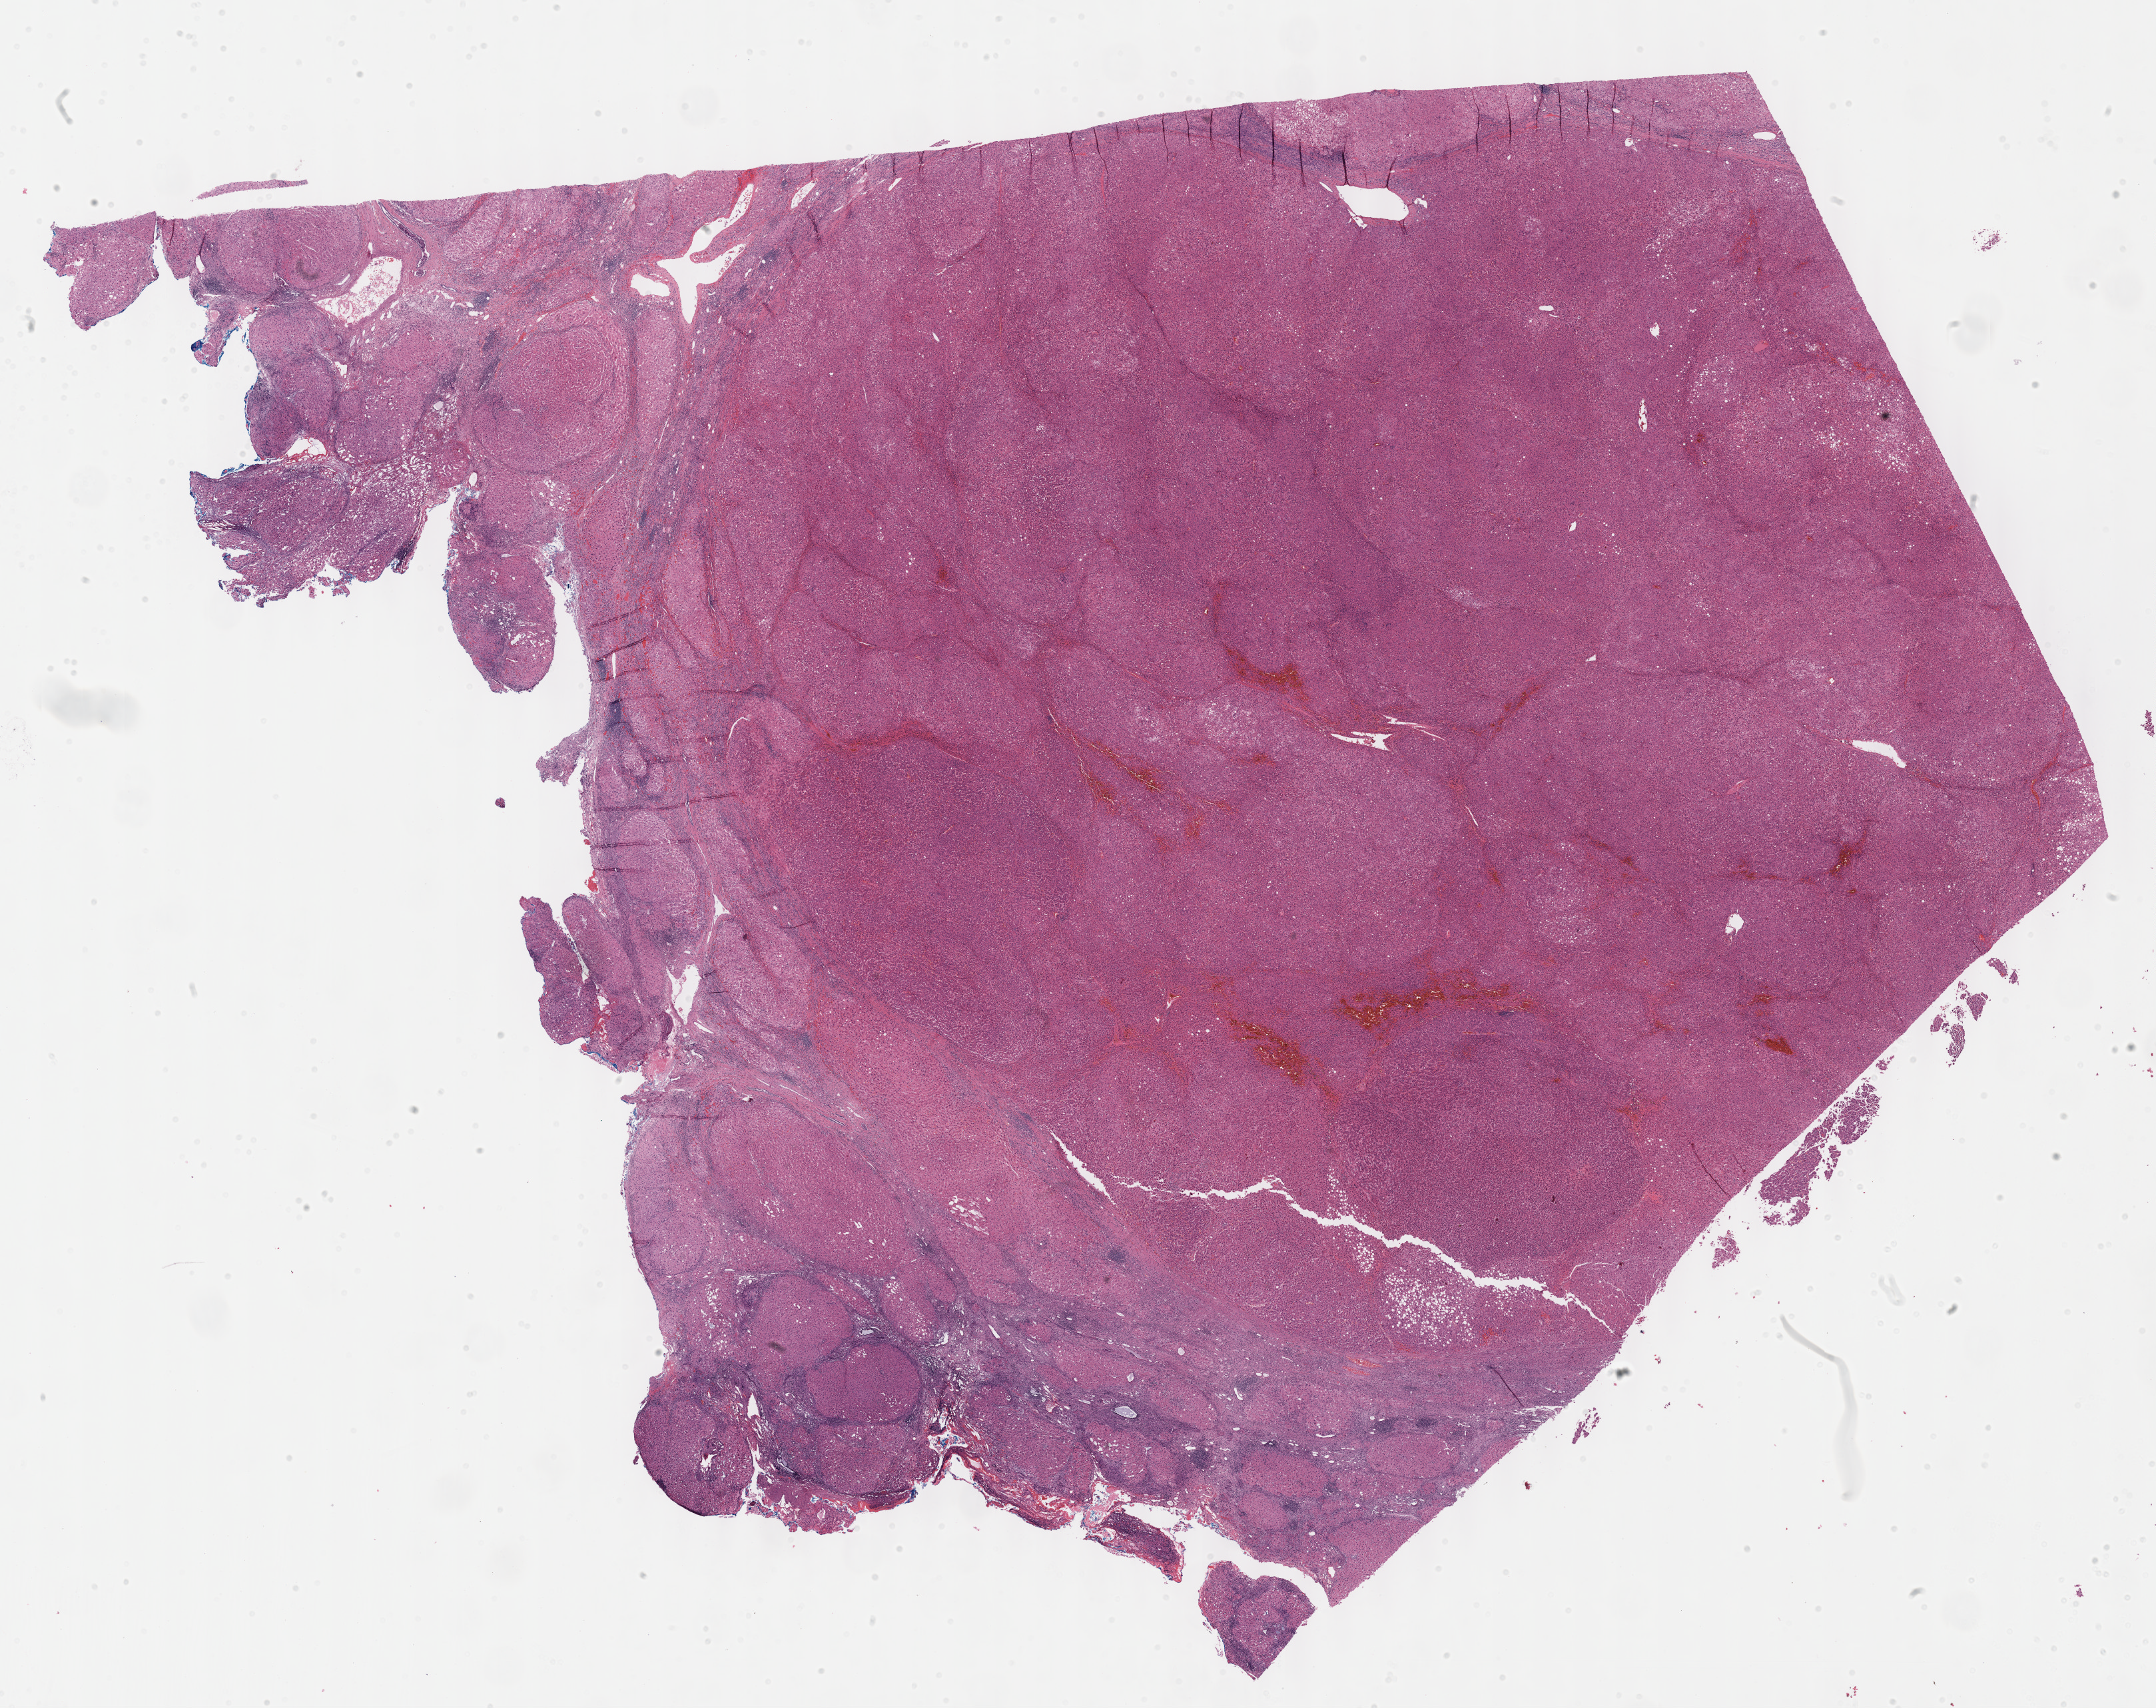
Whole-slide histology image, Hematoxylin and eosin (H&E) stained — a low-resolution overview of the entire scanned area, about 26.2 x 20.7 mm (from a 40x scan); FFPE section; sample: primary tumour, liver. Male patient; age at initial diagnosis 58 years. Histologic grade: G1 (well differentiated).
AJCC pathologic stage: I. Histologic diagnosis: Hepatocellular carcinoma, NOS.